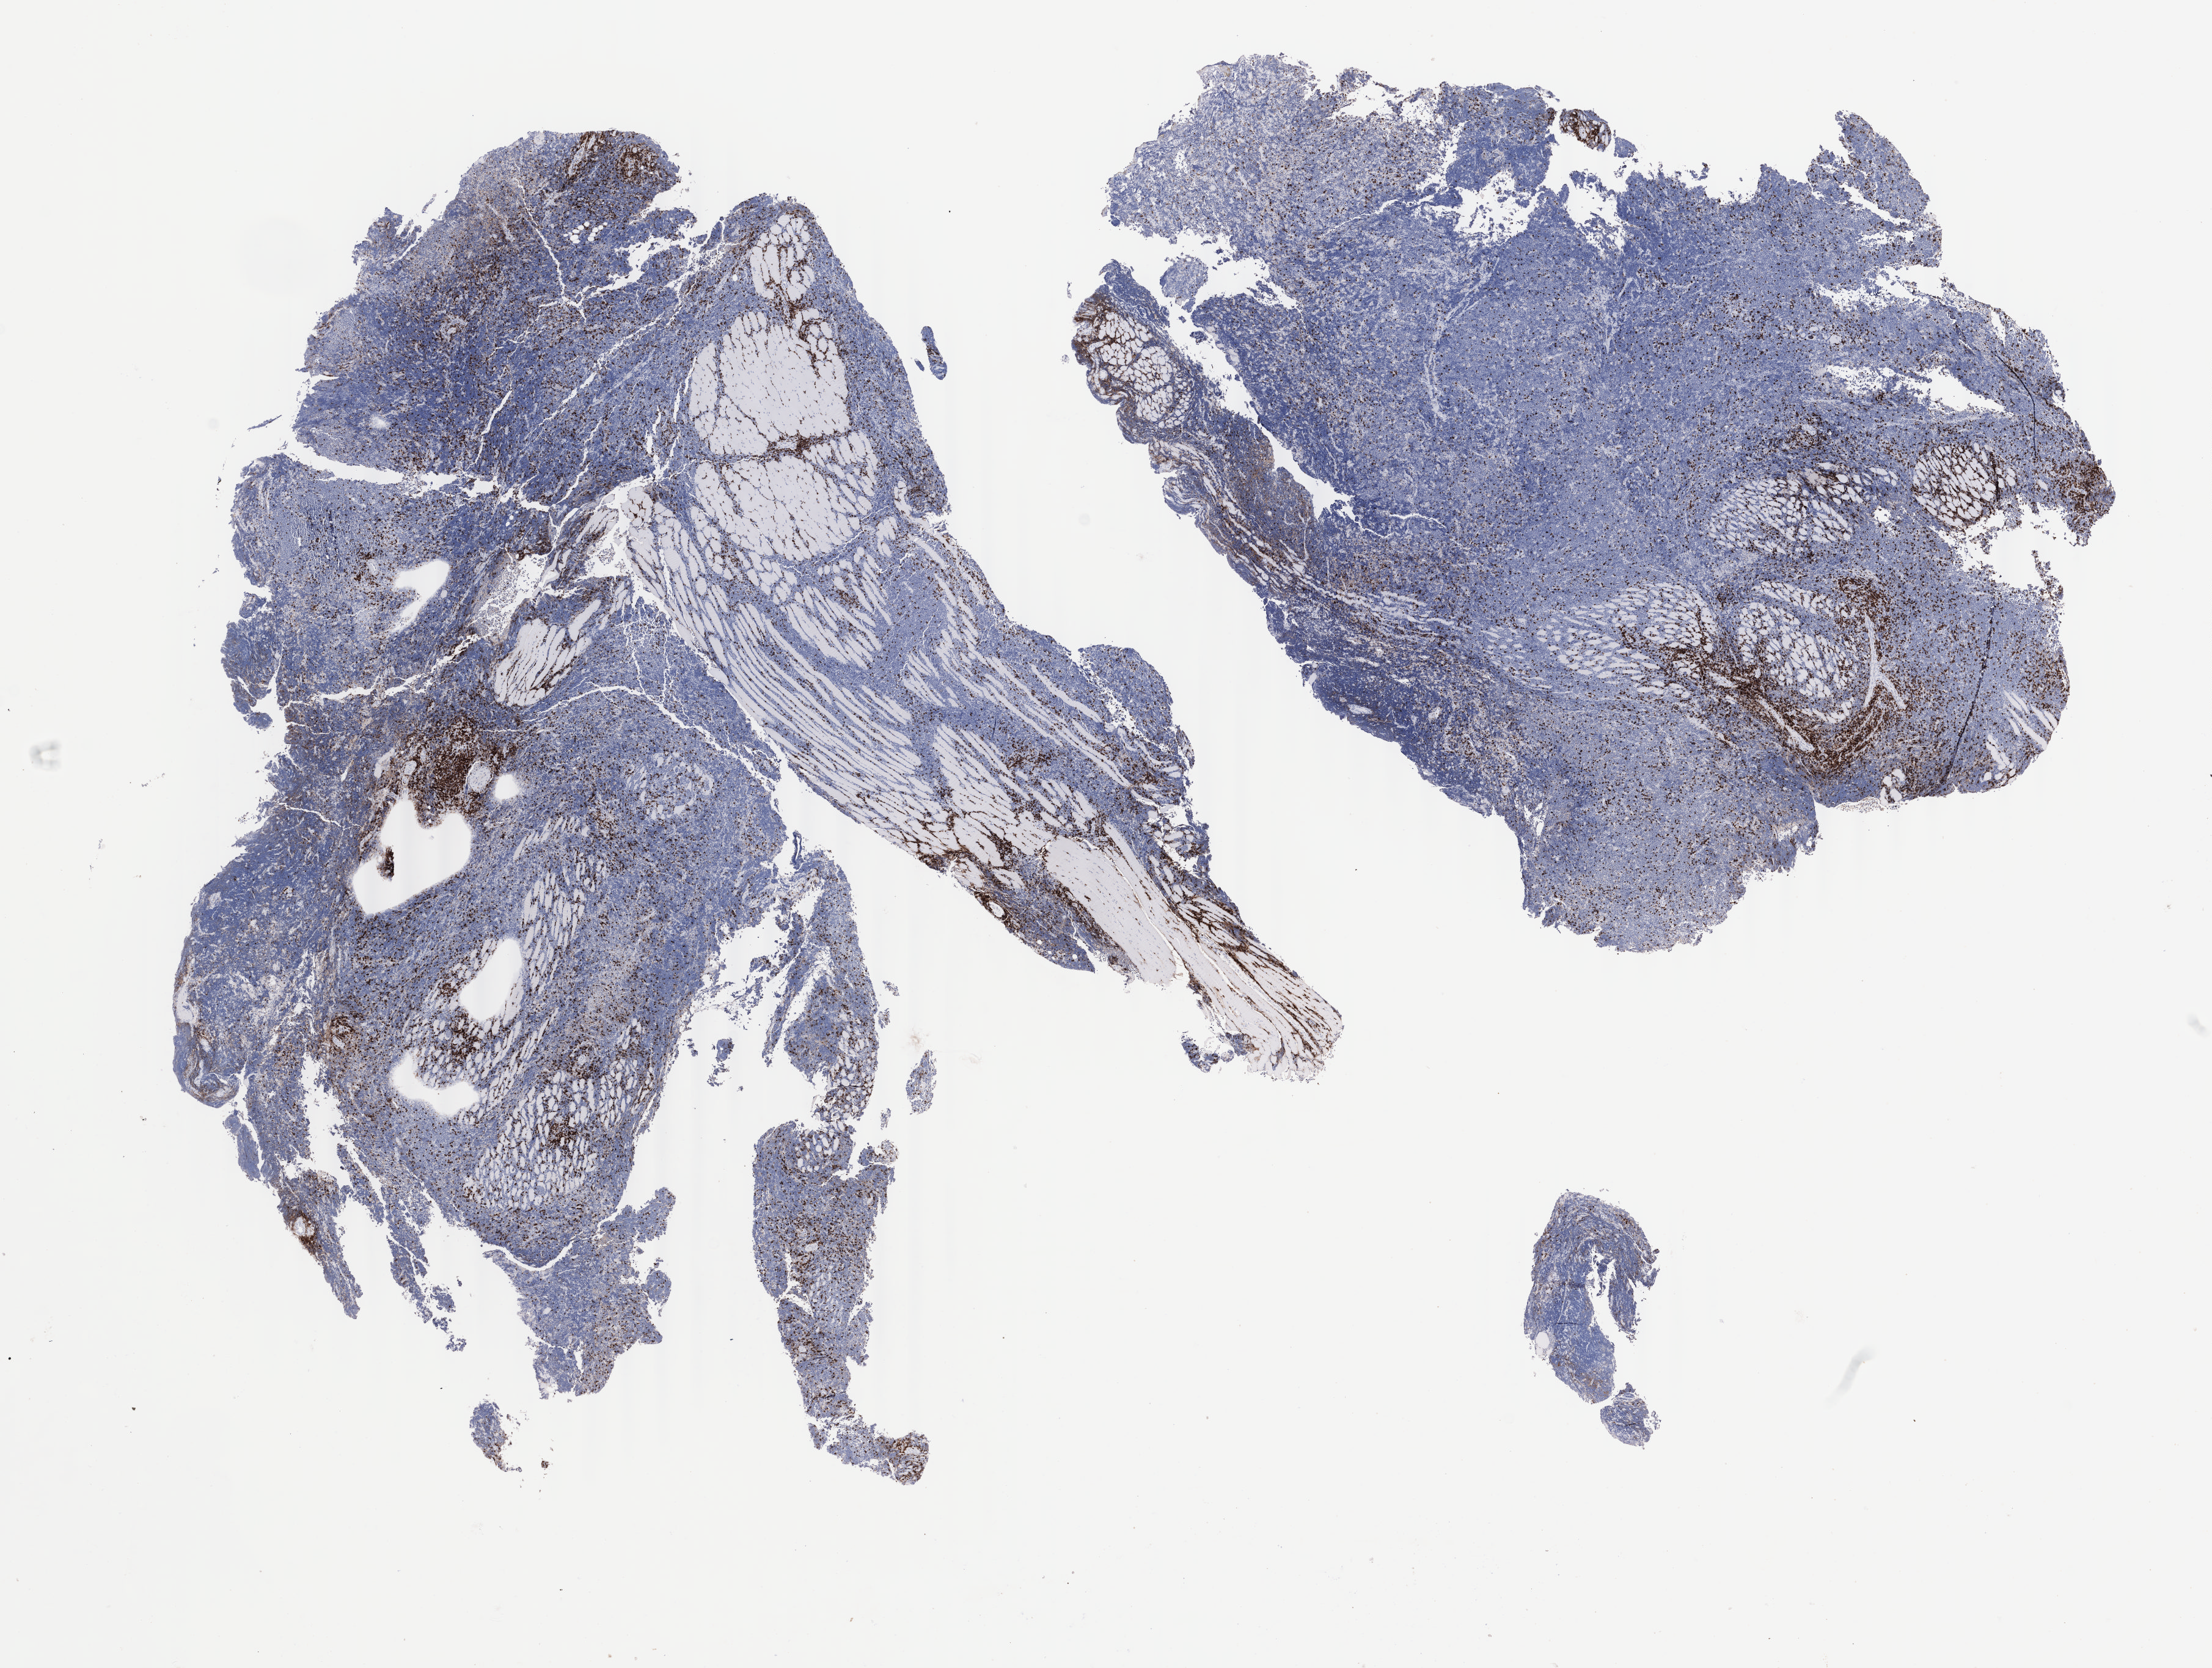
IHC for CD3, whole-slide image, shown as a low-resolution overview of the whole scanned area (about 14.4 x 10.9 mm), specimen: tumor tissue, anatomic site: pelvis. Patient: male, age at initial diagnosis 7 years.
Diagnosis: Diffuse large B-cell lymphoma, NOS.